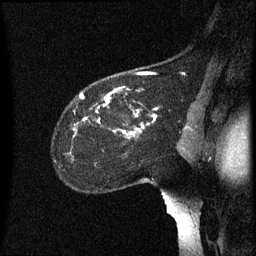
Breast MRI (dynamic contrast-enhanced), one sagittal slice; position 45 of 60 along the scan axis; dynamic contrast-enhanced series, image 2 of 3 at this slice position (ordered by acquisition); 1.5 T; TE 4.2 ms, TR 8.4 ms; 2.2 mm slice thickness; 256 × 256 image matrix, field of view 200 × 200 mm. Patient: female, 35 years. From the clinical record (not read from this slice): setting: breast cancer imaged before/during neoadjuvant chemotherapy; receptor status: HER2-positive.
Structures marked on this image (semi-automatic segmentation, software-assisted and operator-edited):
- analysis volume of interest (the breast-tissue region the enhancement analysis was run in; not a lesion): bounding box <53,72,160,167> (left, top, right, bottom; pixels)
- tumour enhancement mask (voxels above the 70 % enhancement threshold inside the analysis volume of interest): <81,90,158,135>